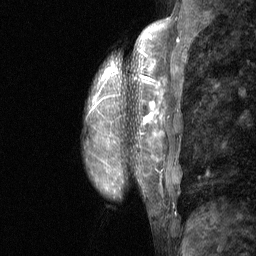
Breast MRI (dynamic contrast-enhanced), one sagittal slice. Position 18 of 64 along the scan axis. Dynamic contrast-enhanced study with each time point stored as its own series, time point 2 of 3 at this slice position (early post-contrast, ordered by acquisition time). 1.5 T. TE 4.8 ms, TR 27 ms. 2 mm slice thickness. 256 × 256 image matrix. Female patient, age 36 years. Case-level facts recorded for this patient, not image findings: setting: breast cancer imaged before/during neoadjuvant chemotherapy; receptor status: HR-positive, HER2-negative.
Annotated regions visible in this slice (semi-automatic segmentation, software-assisted and operator-edited):
- analysis volume of interest (the breast-tissue region the enhancement analysis was run in; not a lesion): box from (x=84, y=12) to (x=211, y=236) px
- tumour enhancement mask (voxels above the 90 % enhancement threshold inside the analysis volume of interest): (x=147, y=35)–(x=163, y=136)